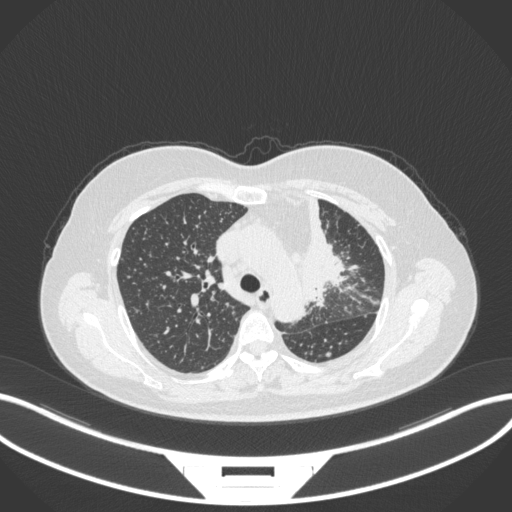
Chest CT, one axial slice; lung window (W 1500 / L -600 HU); 1 mm slice thickness; 512 × 512 image matrix, field of view 400 × 400 mm. Patient: female, 49 years. Case-level facts recorded for this patient, not image findings: clinical TNM (as recorded): T1c N0 M1.
Outlined on this slice (rectangle marked by the reading radiologist):
- lung tumour (recorded histology: adenocarcinoma): bounding box [x1, y1, x2, y2] px = [293, 190, 351, 313]